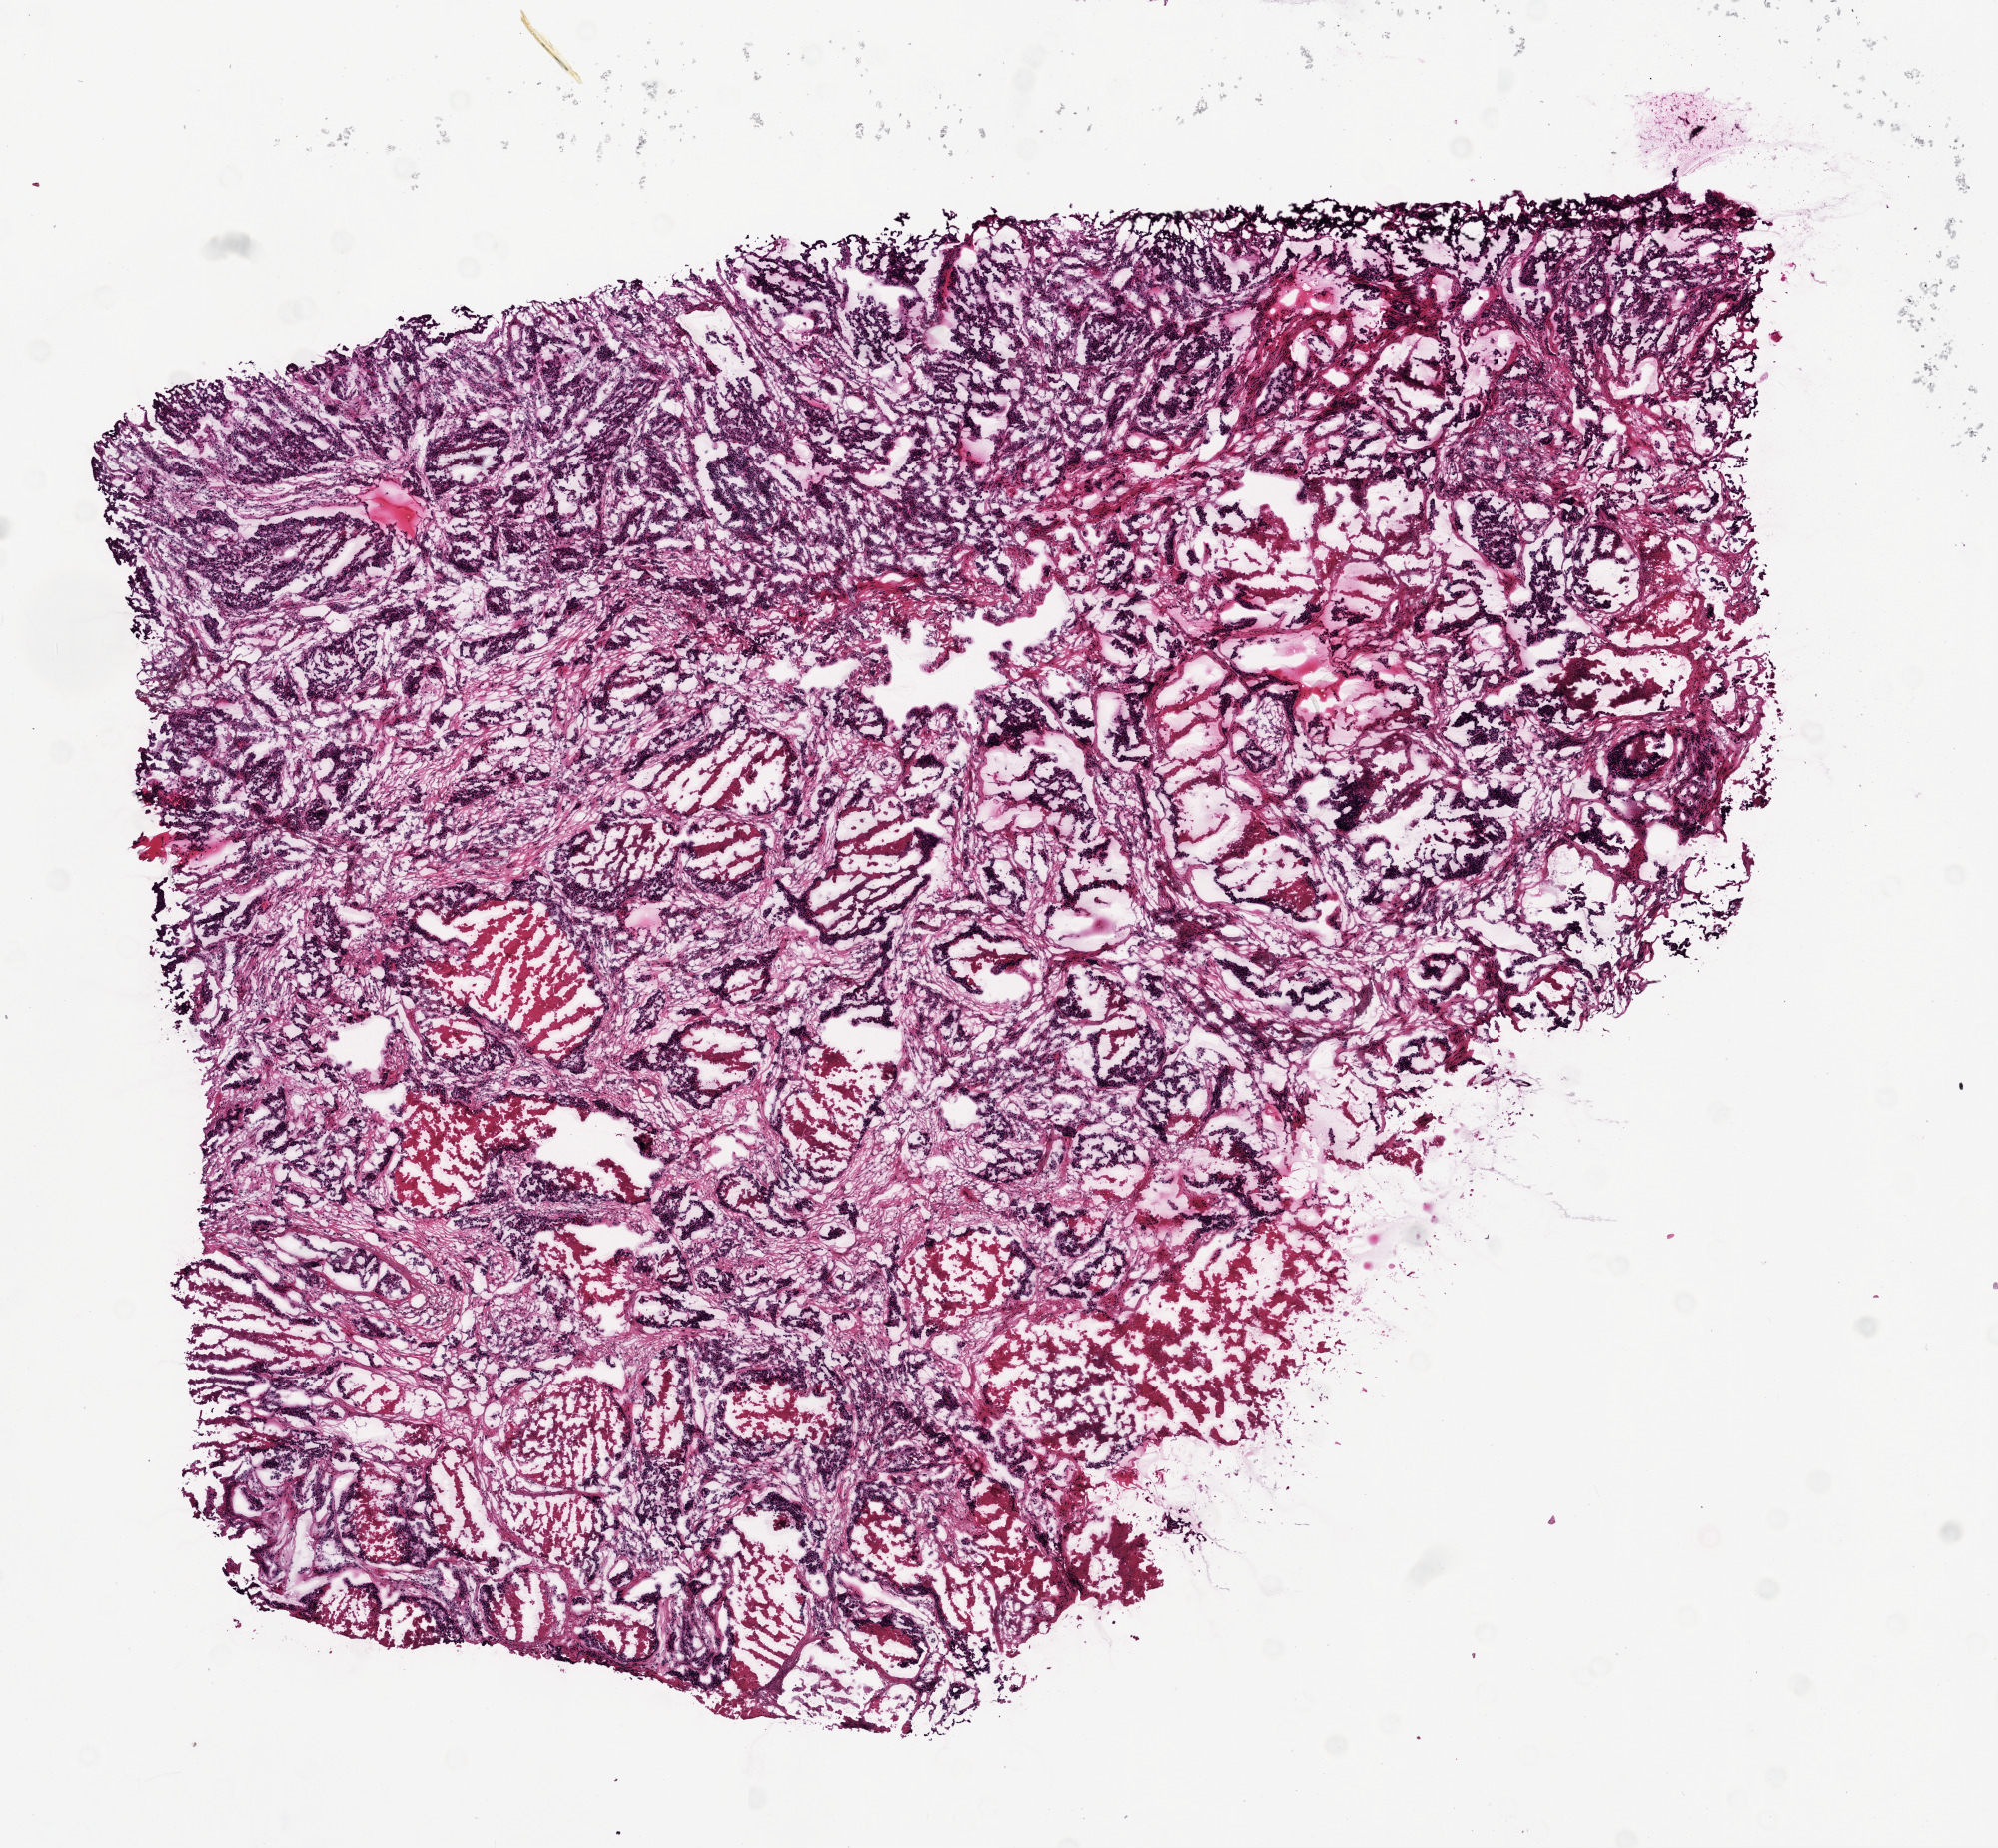
H&E-stained whole-slide image — shown as a low-resolution overview of the whole scanned area (about 8.0 x 7.4 mm, from a 20x scan); frozen section from the top of the tissue portion; primary tumour sample from the lung. Patient: female, age at initial diagnosis 70 years. Pathologist review of this section (percent, as recorded): tumour cells 40%, tumour nuclei 85%, normal cells 0%, stromal cells 57%, necrosis 3%.
• laterality: right
• diagnosis: Adenocarcinoma, NOS (upper lobe, lung)